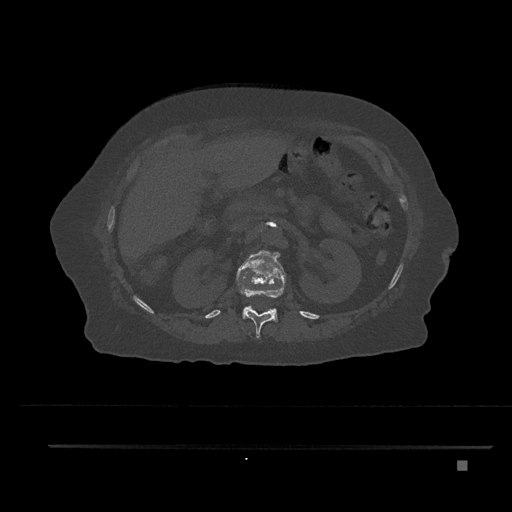
CT including the spine, one axial slice. Slice 243 of 797 in the series (ordered by position). Reconstruction kernel Br40s/3. 120 kVp. Bone window (W 1800 / L 400 HU). 0.5 mm slice thickness. 512 × 512 image matrix. Patient: female, 76 years. From the clinical record (not read from this slice): primary cancer: lung; vertebrae with lytic lesions (as recorded): T11, L3.
Outlined on this slice (semi-automatic segmentation, software-assisted and operator-edited):
- L1 vertebra: bounding box [x1, y1, x2, y2] px = [237, 250, 286, 322]
- T12 vertebra: [240, 283, 279, 338]